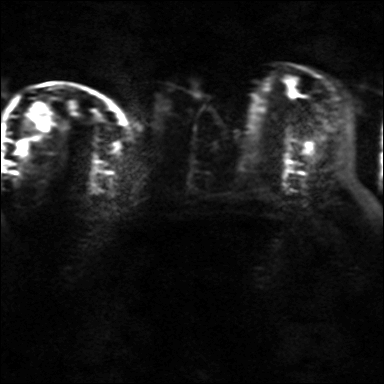
Breast MRI, one axial slice. Slice 17 of 36 in the series (ordered by position). Diffusion-weighted series; image 2 of 4 stored at this slice position (different b-values; order by instance number). 3 T. 4 mm slice thickness. 384 × 384 image matrix. Female patient.
Structures marked on this image (expert manual segmentation):
- tumour on diffusion-weighted imaging: bounding box [x1, y1, x2, y2] px = [19, 141, 27, 153]